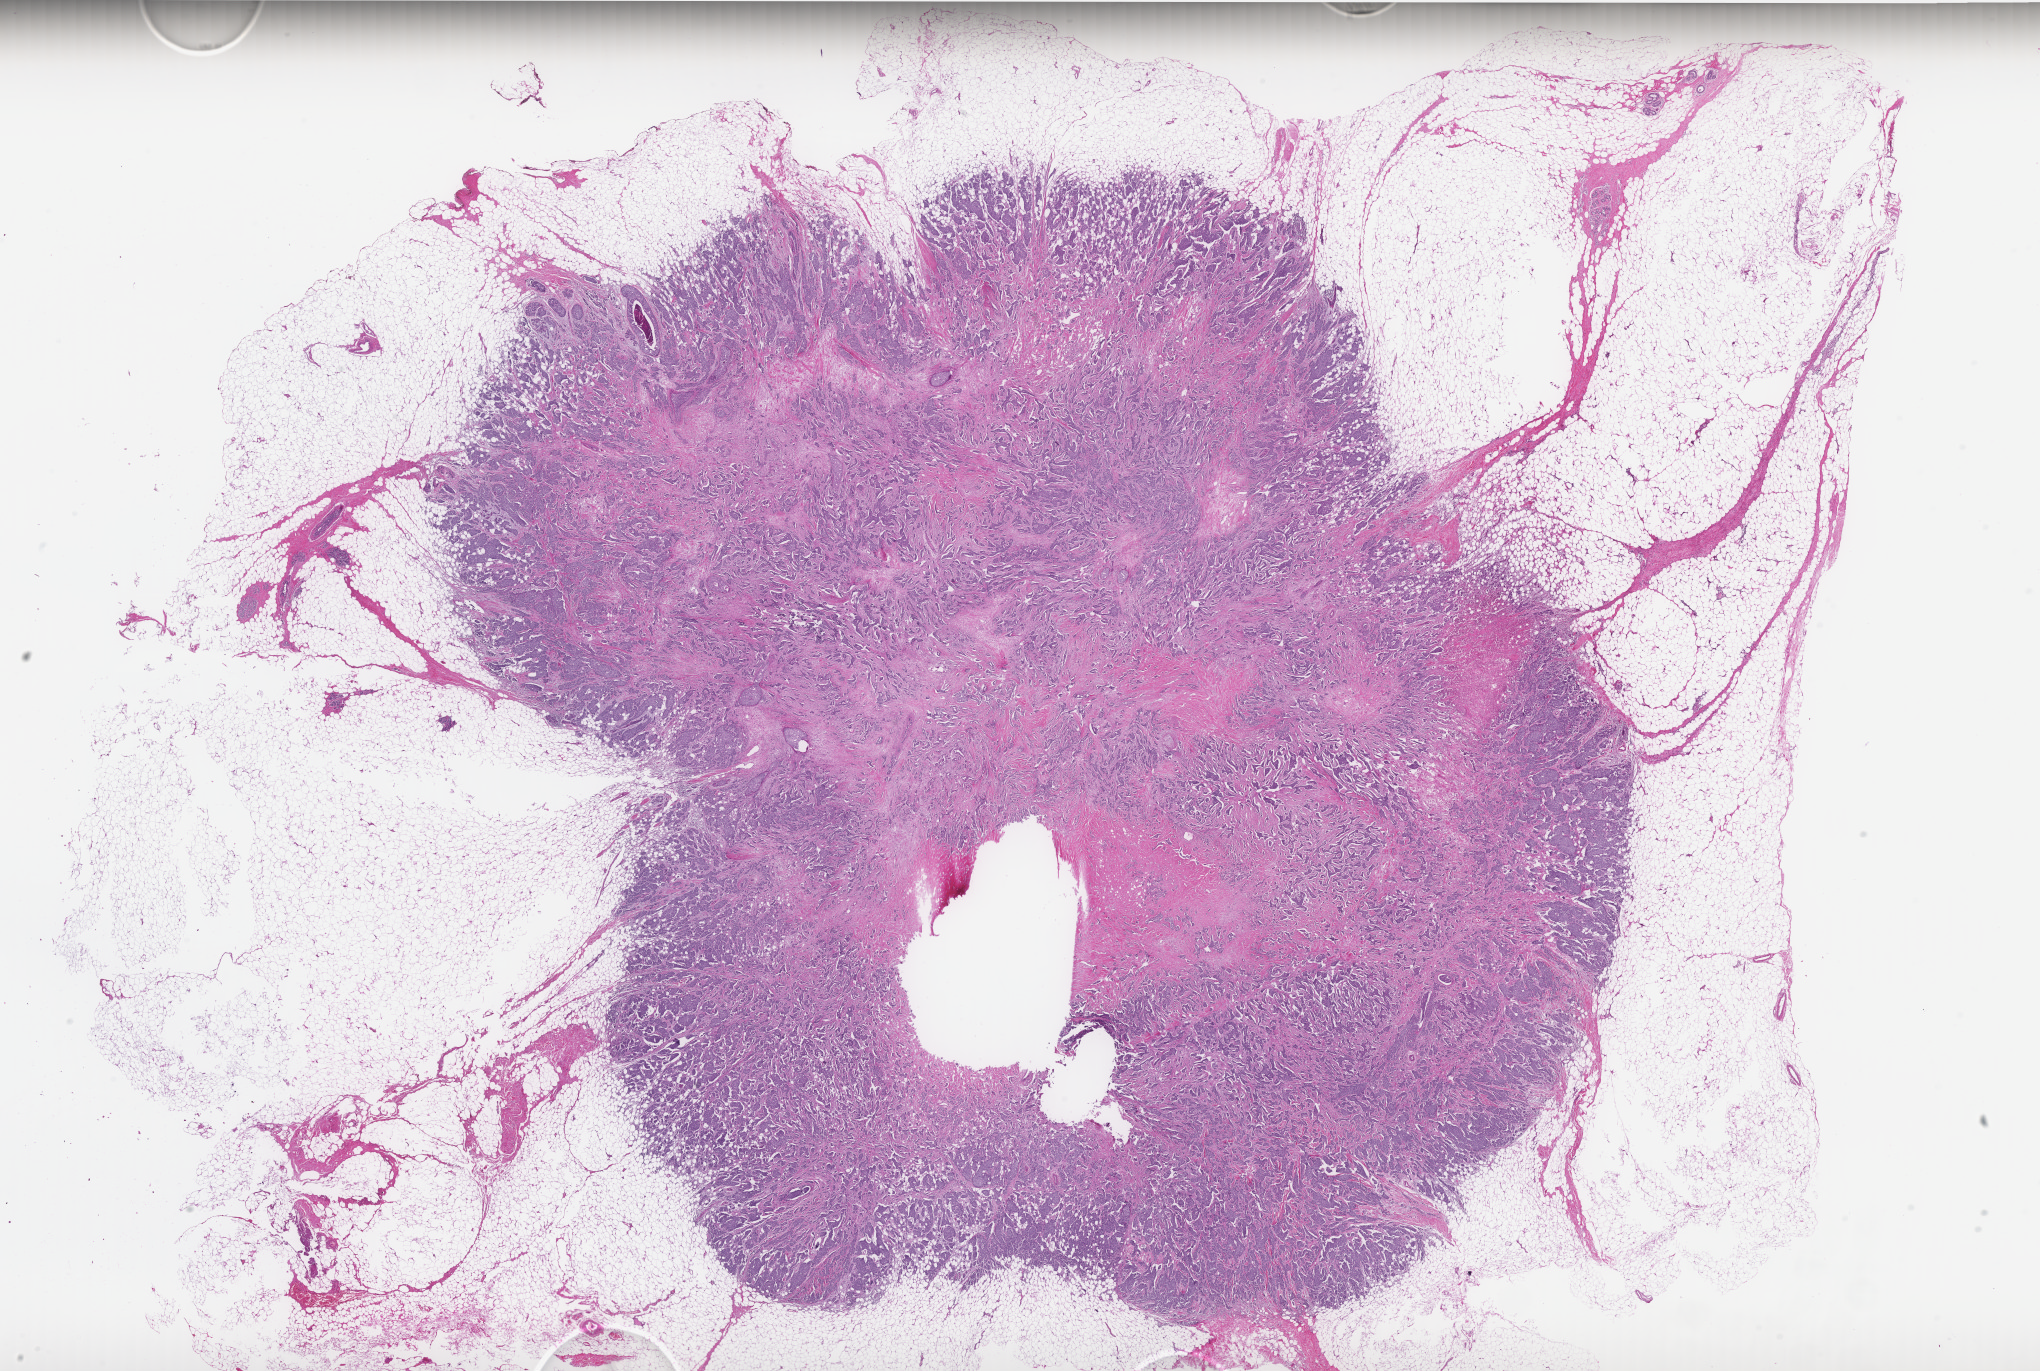
Whole-slide histology image, Hematoxylin and eosin (H&E) stained, low-resolution overview of the scanned area, about 32.7 x 22.0 mm (slide scanned at 40x); formalin-fixed paraffin-embedded (FFPE) diagnostic section; breast, primary tumour sample. Female patient; age at initial diagnosis 39 years.
• lymph nodes positive (case pathology): 0 of 2 examined
• histologic diagnosis: Infiltrating duct carcinoma, NOS
• AJCC pathologic stage: IIA (6th edition)